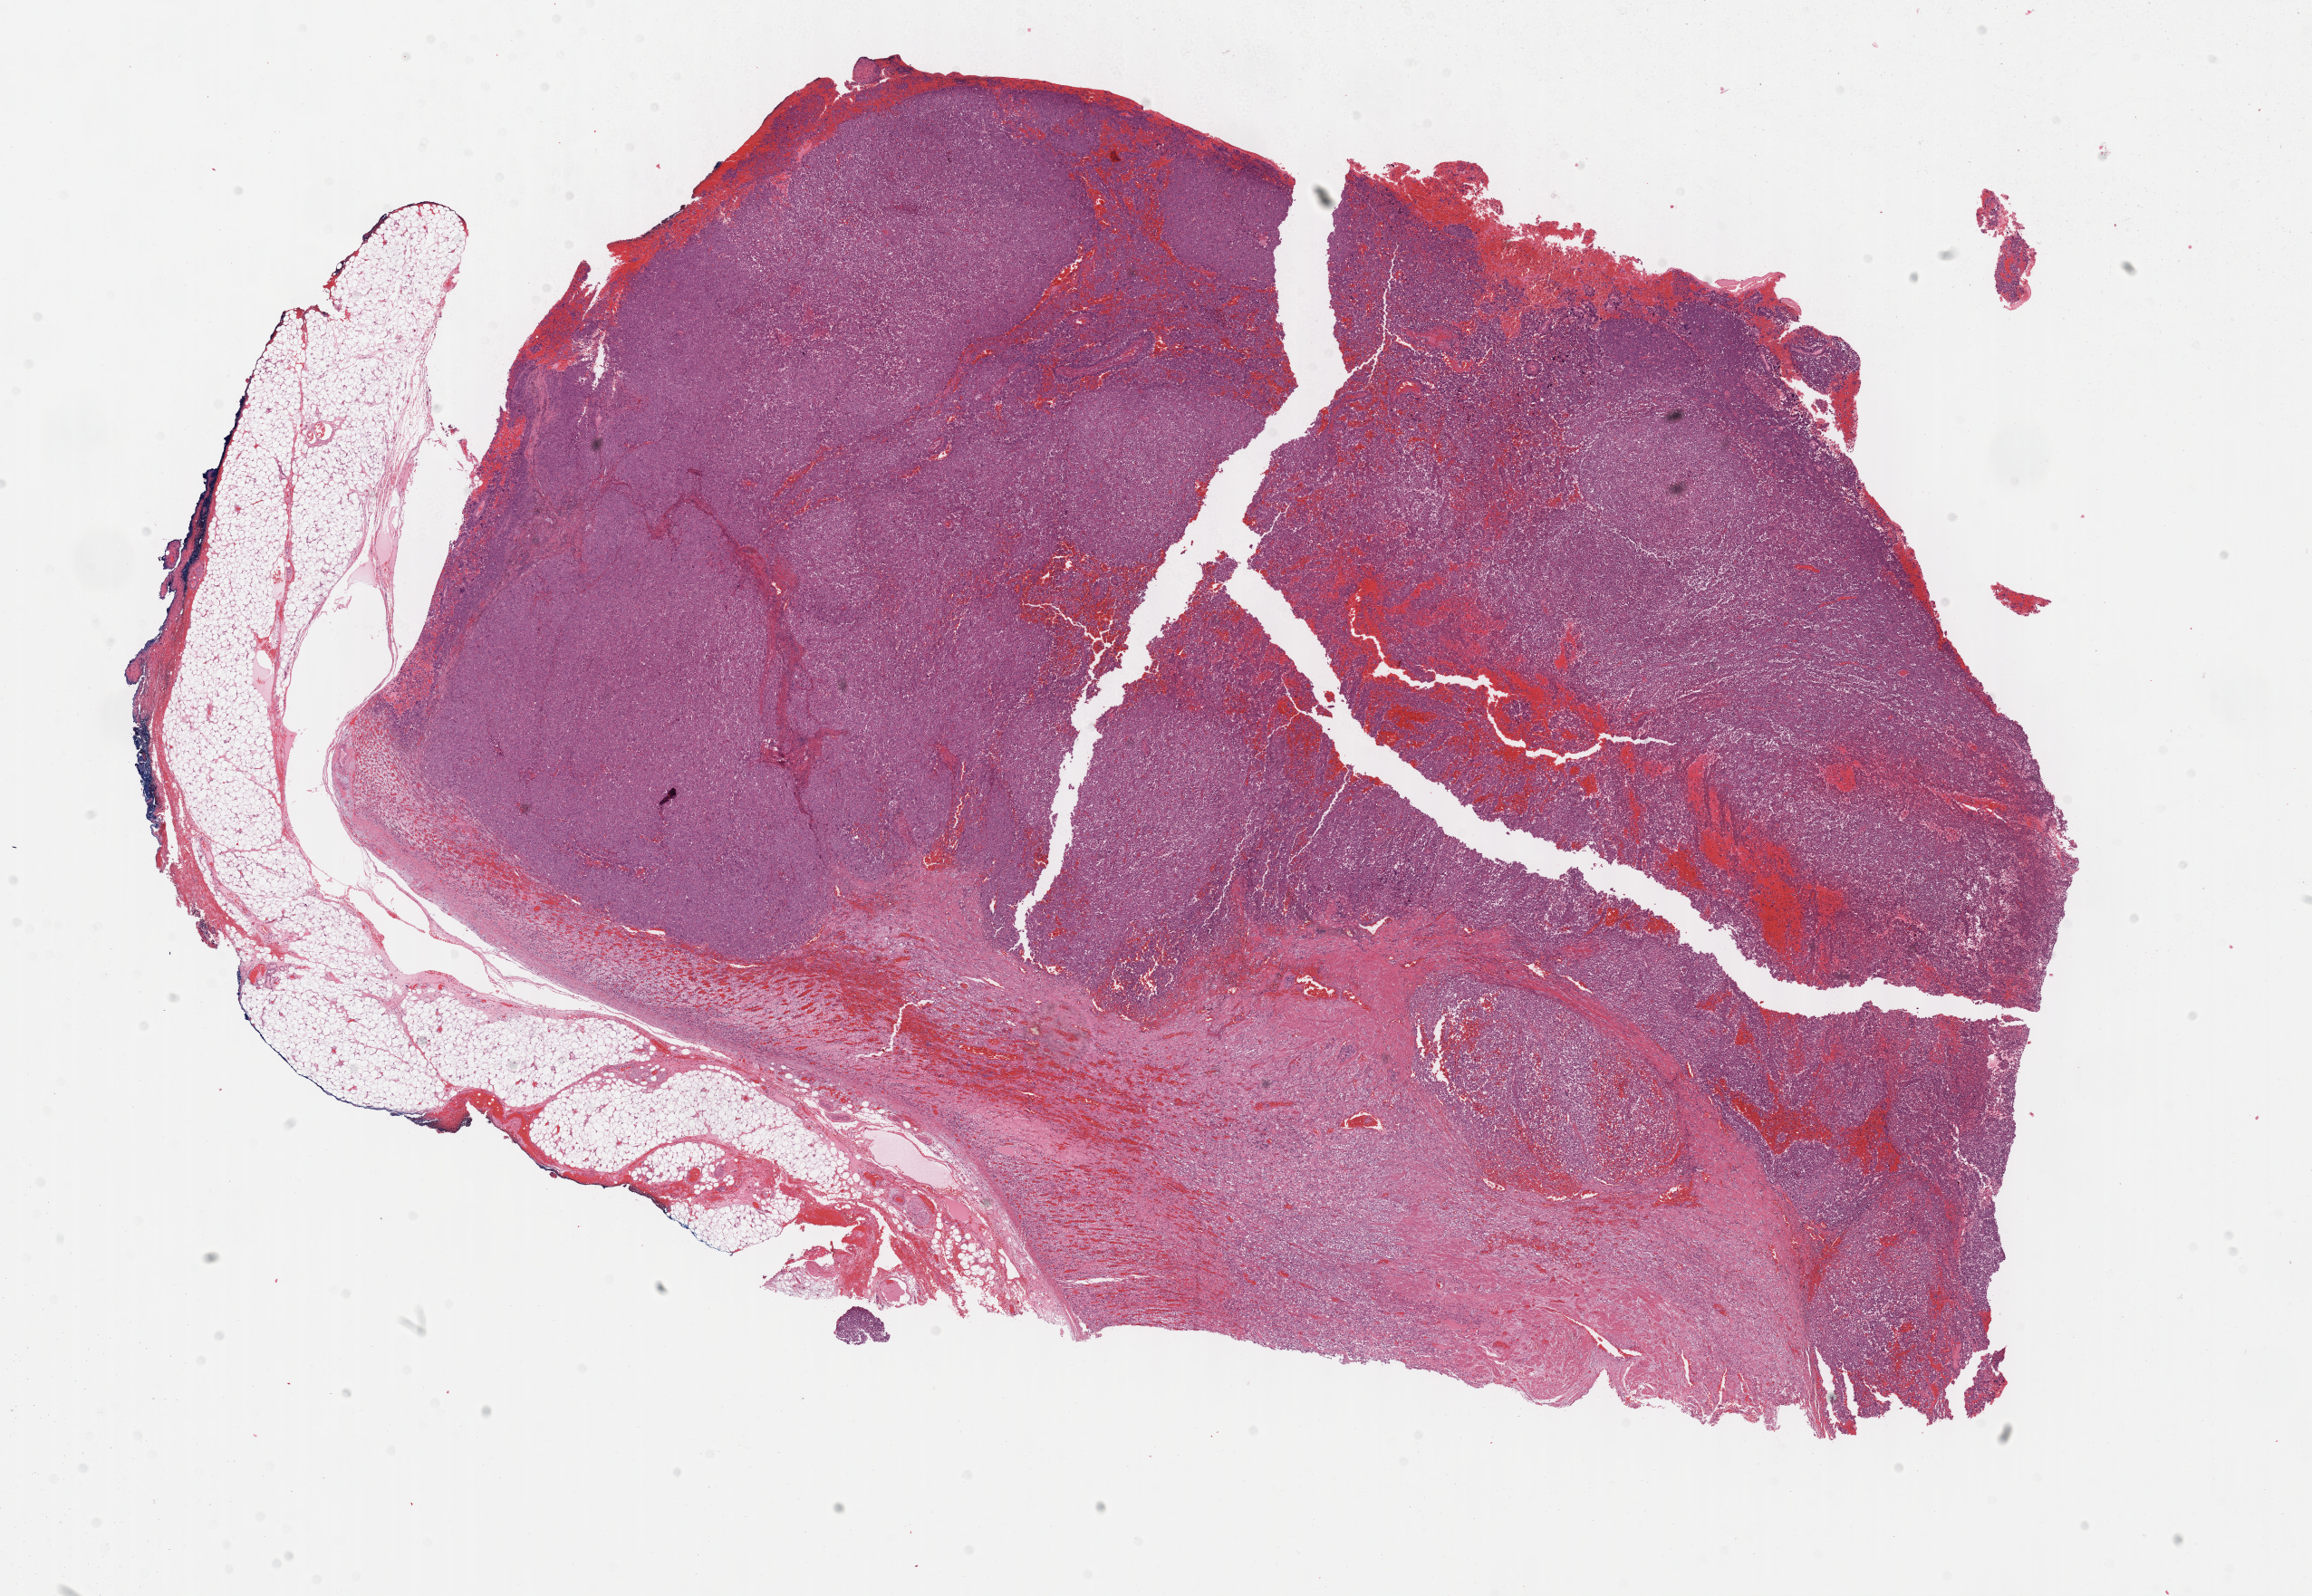
H&E-stained whole-slide image, low-resolution overview of the scanned area, about 20.6 x 14.2 mm. Formalin-fixed paraffin-embedded (FFPE) diagnostic section. Sample: primary tumour, adrenal cortex. Patient: male, age at initial diagnosis 52 years.
• histologic diagnosis: Adrenal cortical carcinoma (cortex of adrenal gland)